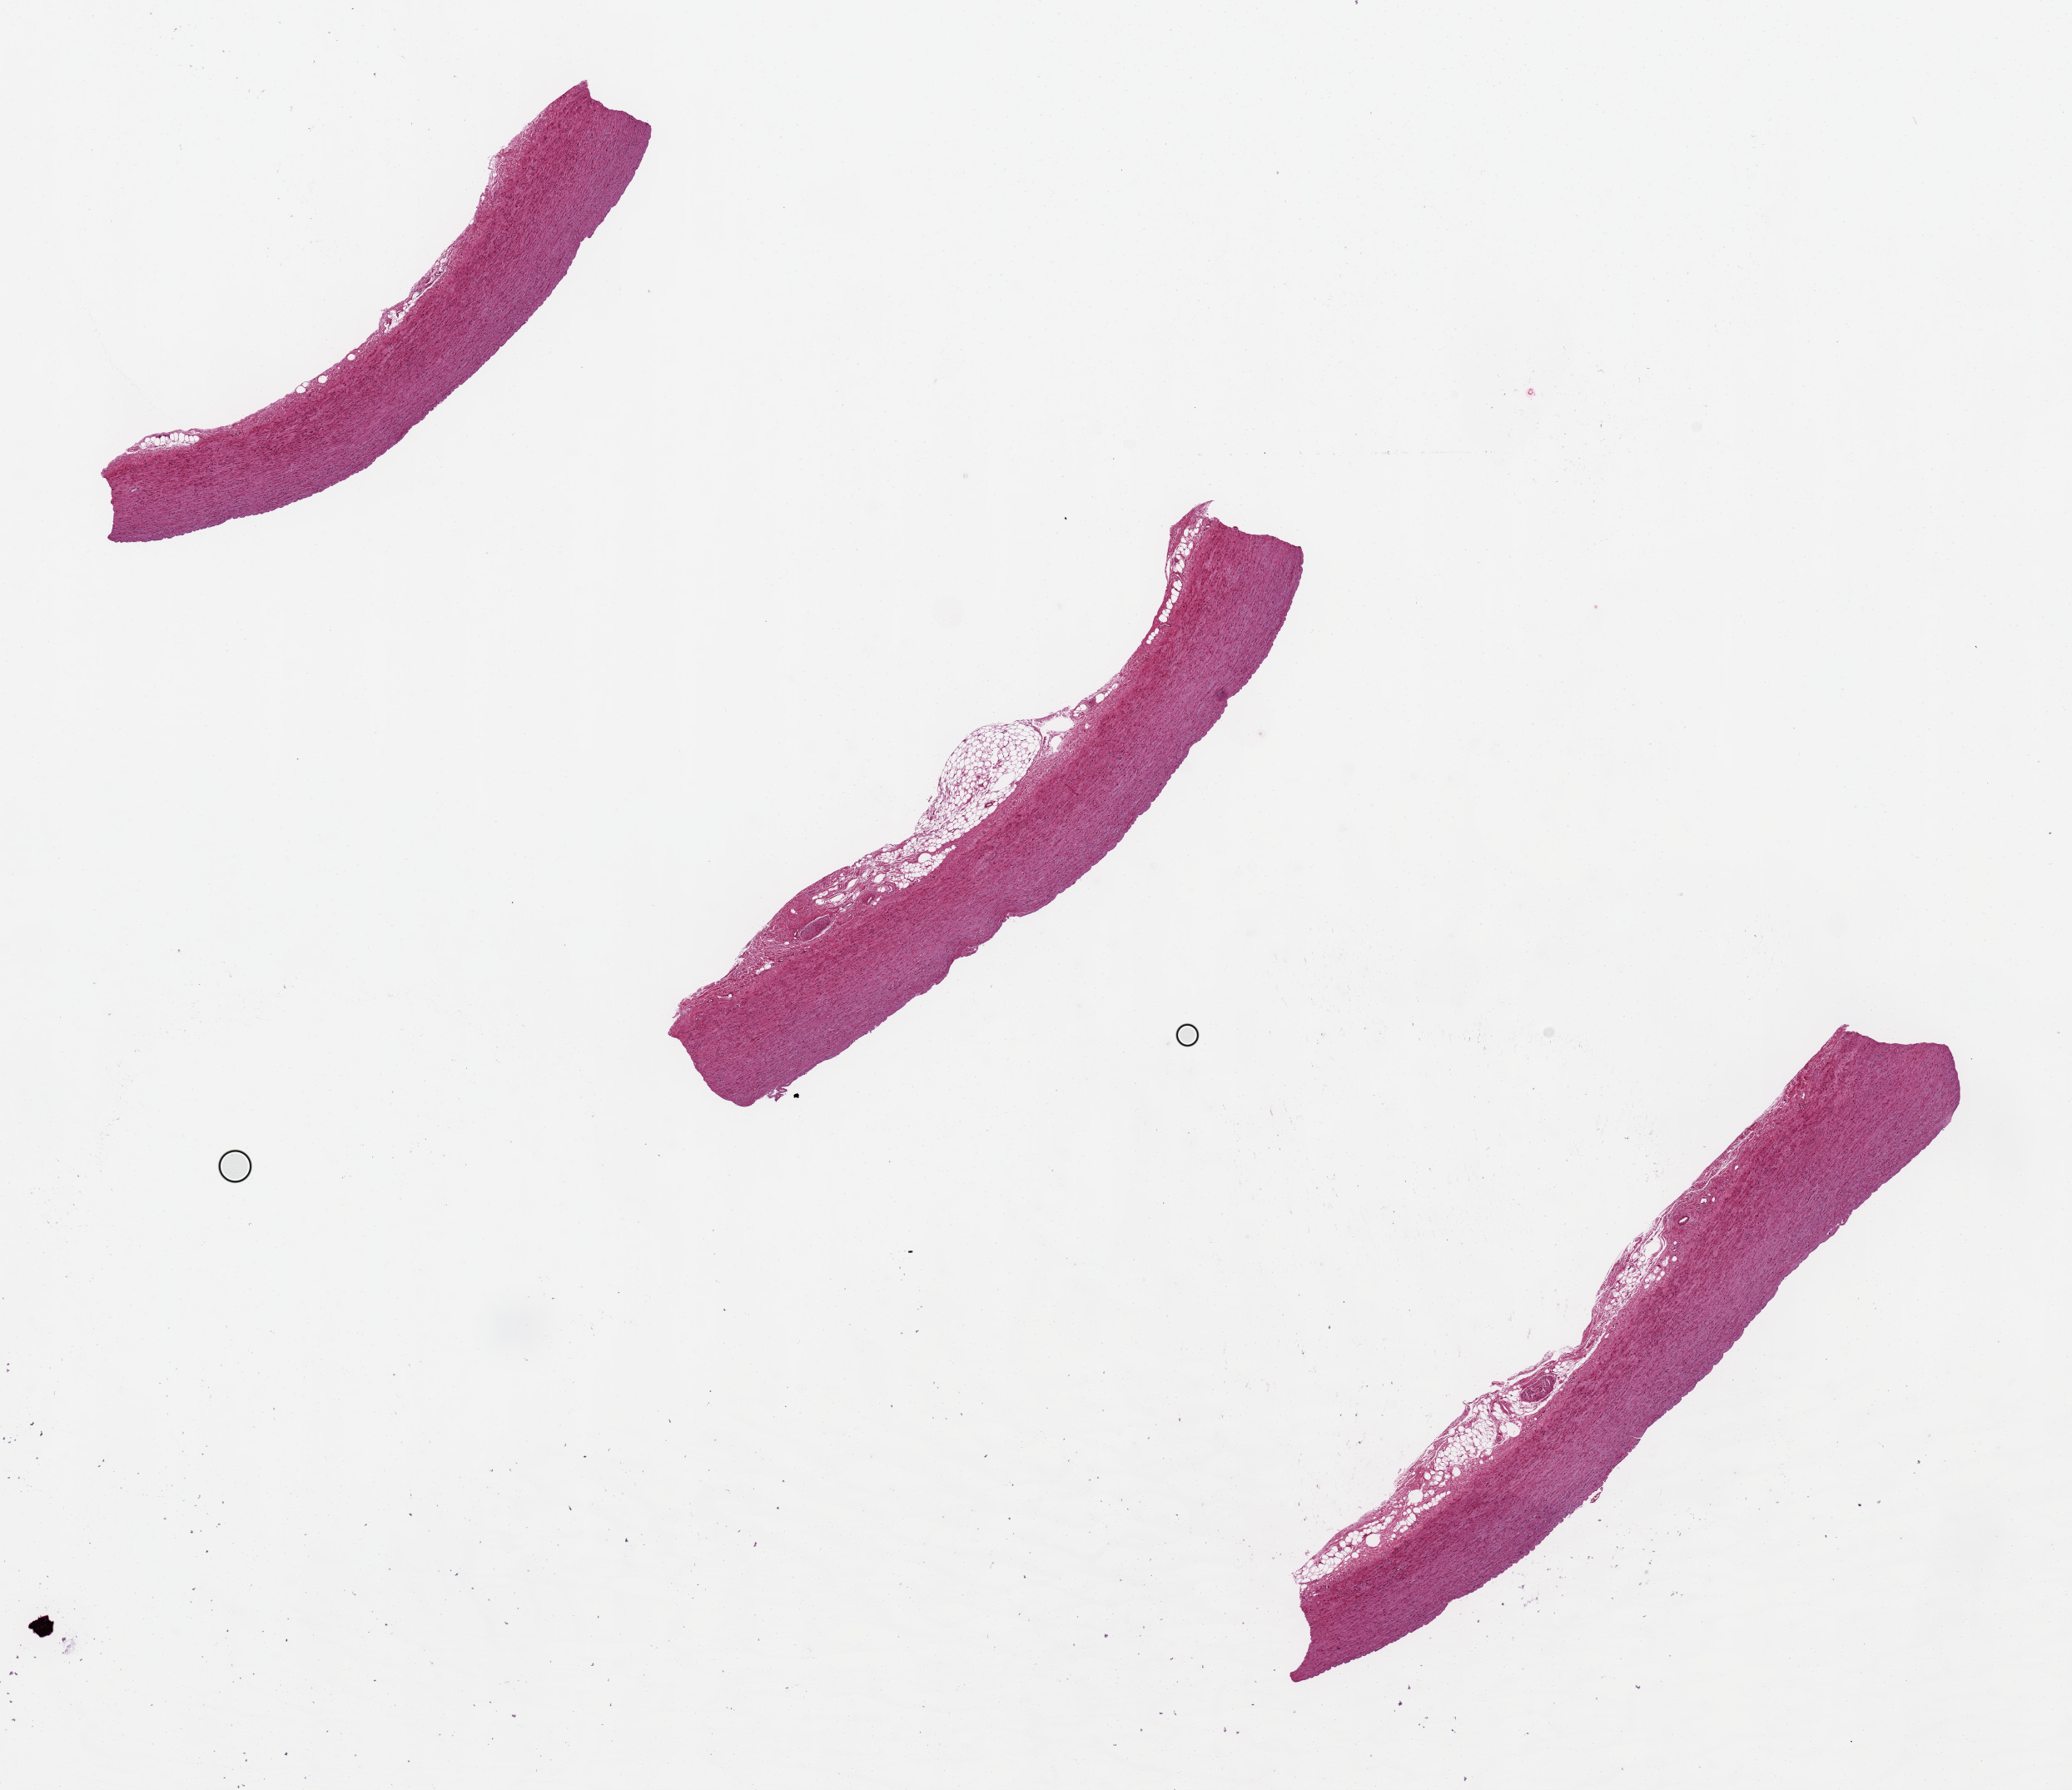
Whole-slide image, haematoxylin and eosin stain — a low-resolution overview of the entire scanned area, about 19.7 x 17.0 mm, PAXgene-fixed, paraffin-embedded tissue, target tissue: aorta, tissue donor sample. Donor: male.
- reviewer comment on this tissue sample: Endothelium partially sloughed